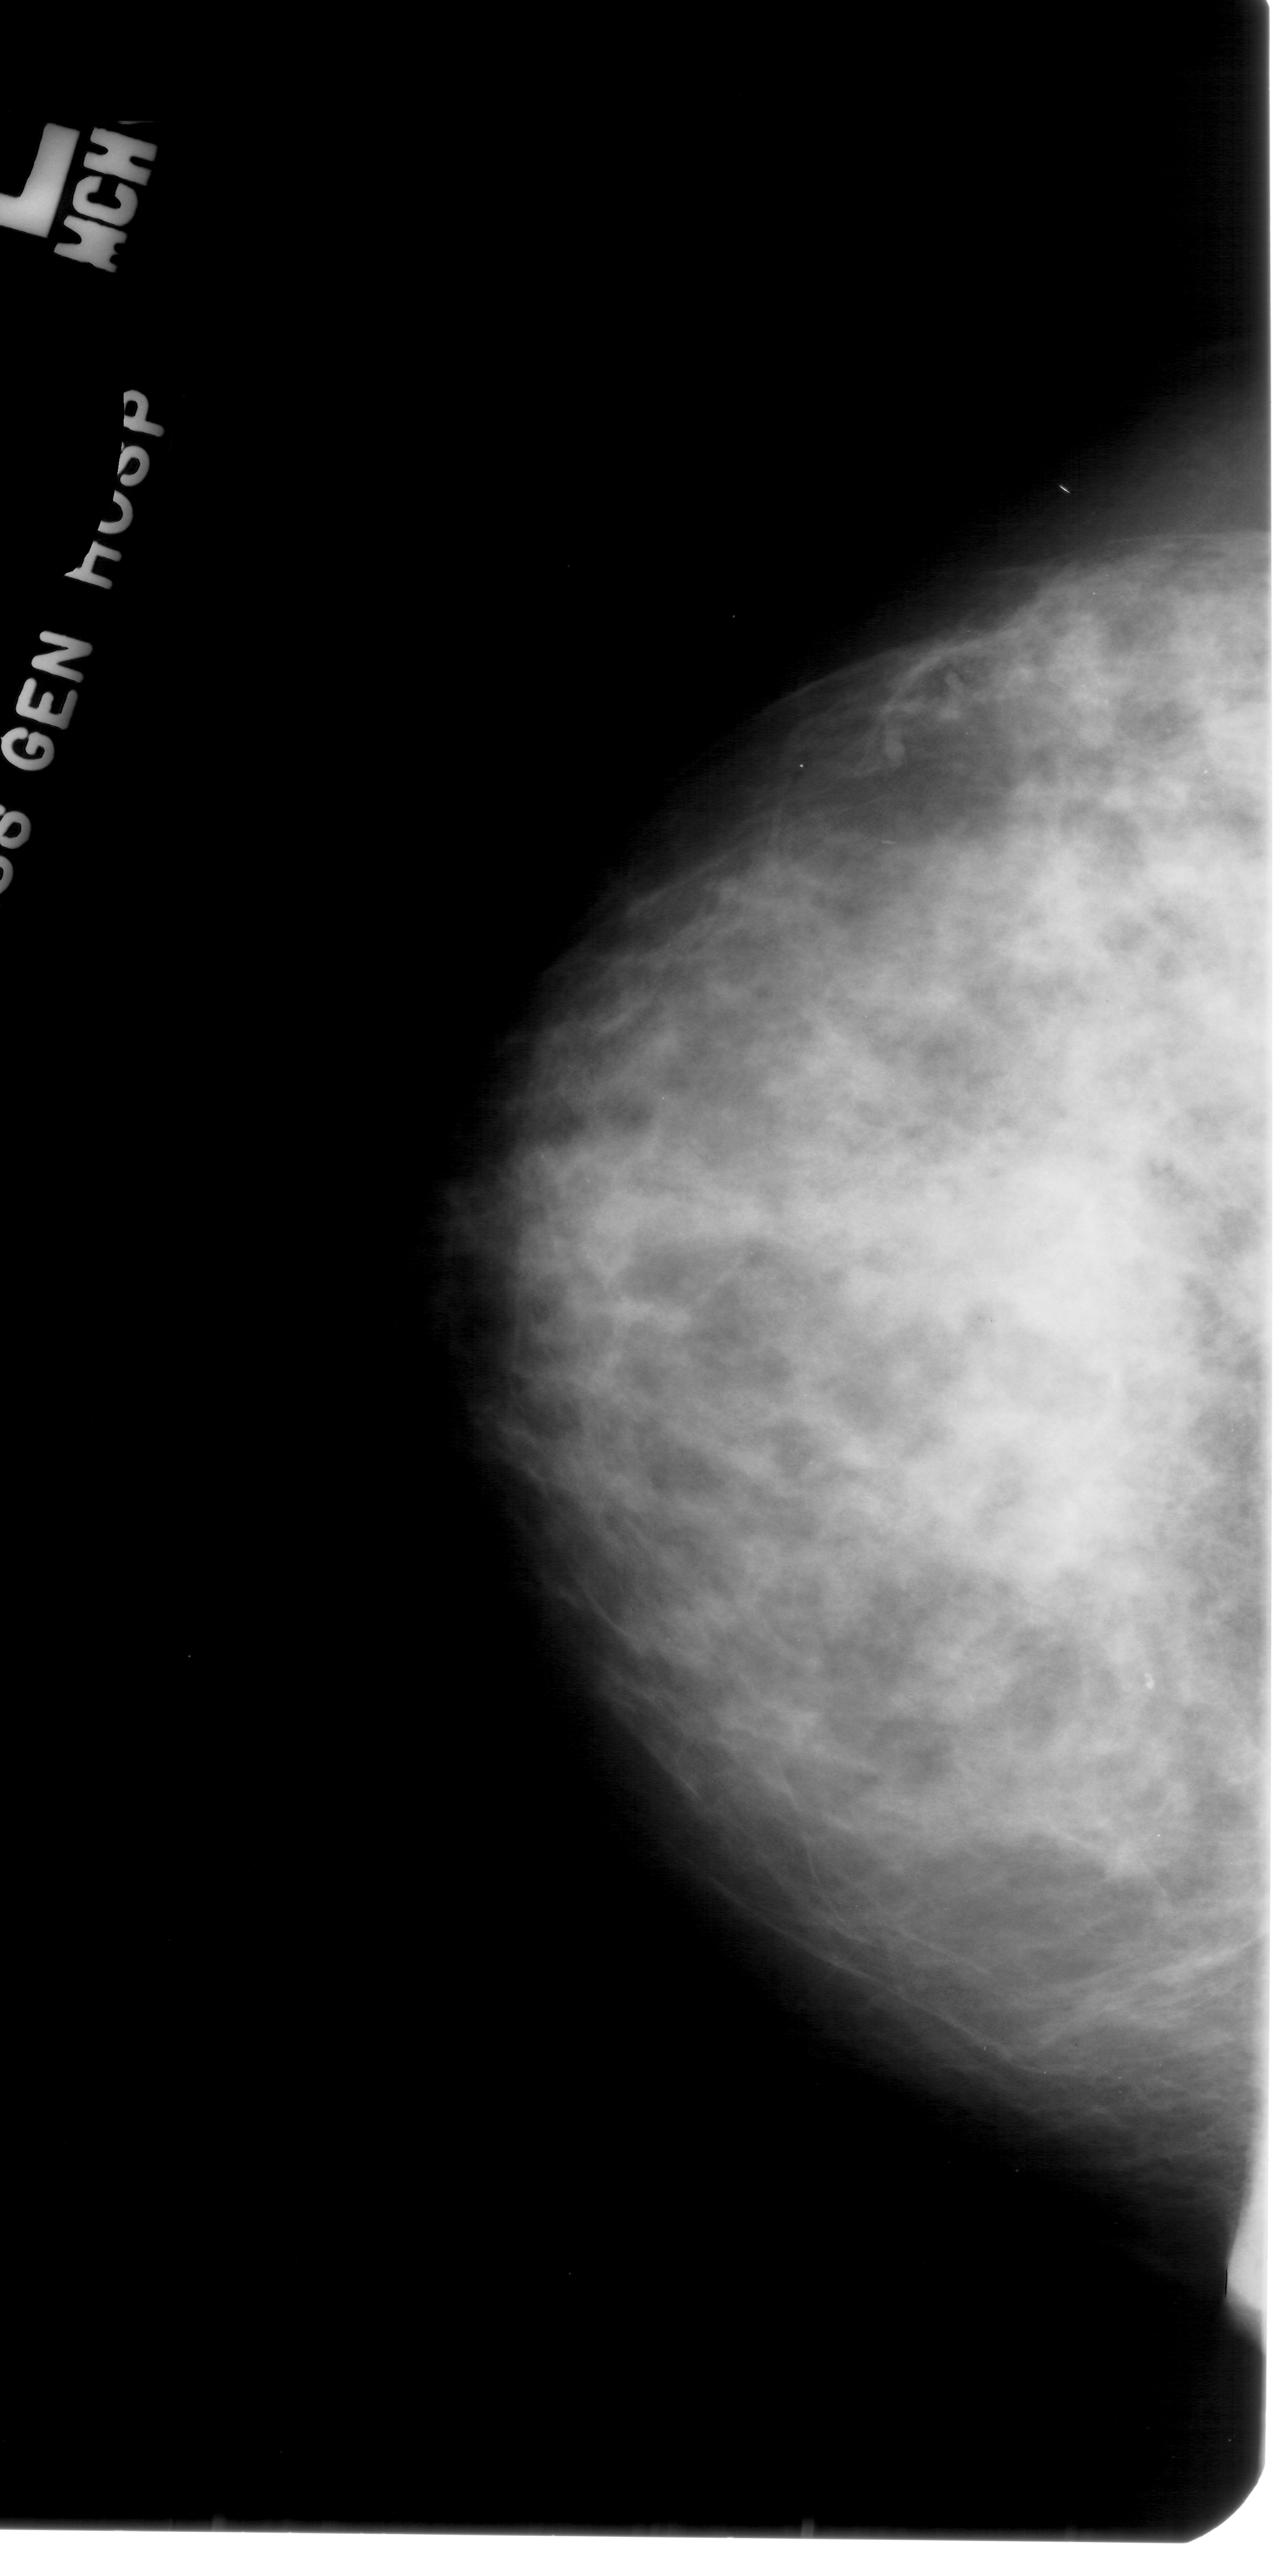
Scanned film-screen mammogram, left breast, craniocaudal (CC) view, BI-RADS breast density category 3 (scale 1–4).
Abnormality record for this image: calcifications, morphology pleomorphic, distribution clustered; BI-RADS assessment category 4; pathology (as recorded): benign.